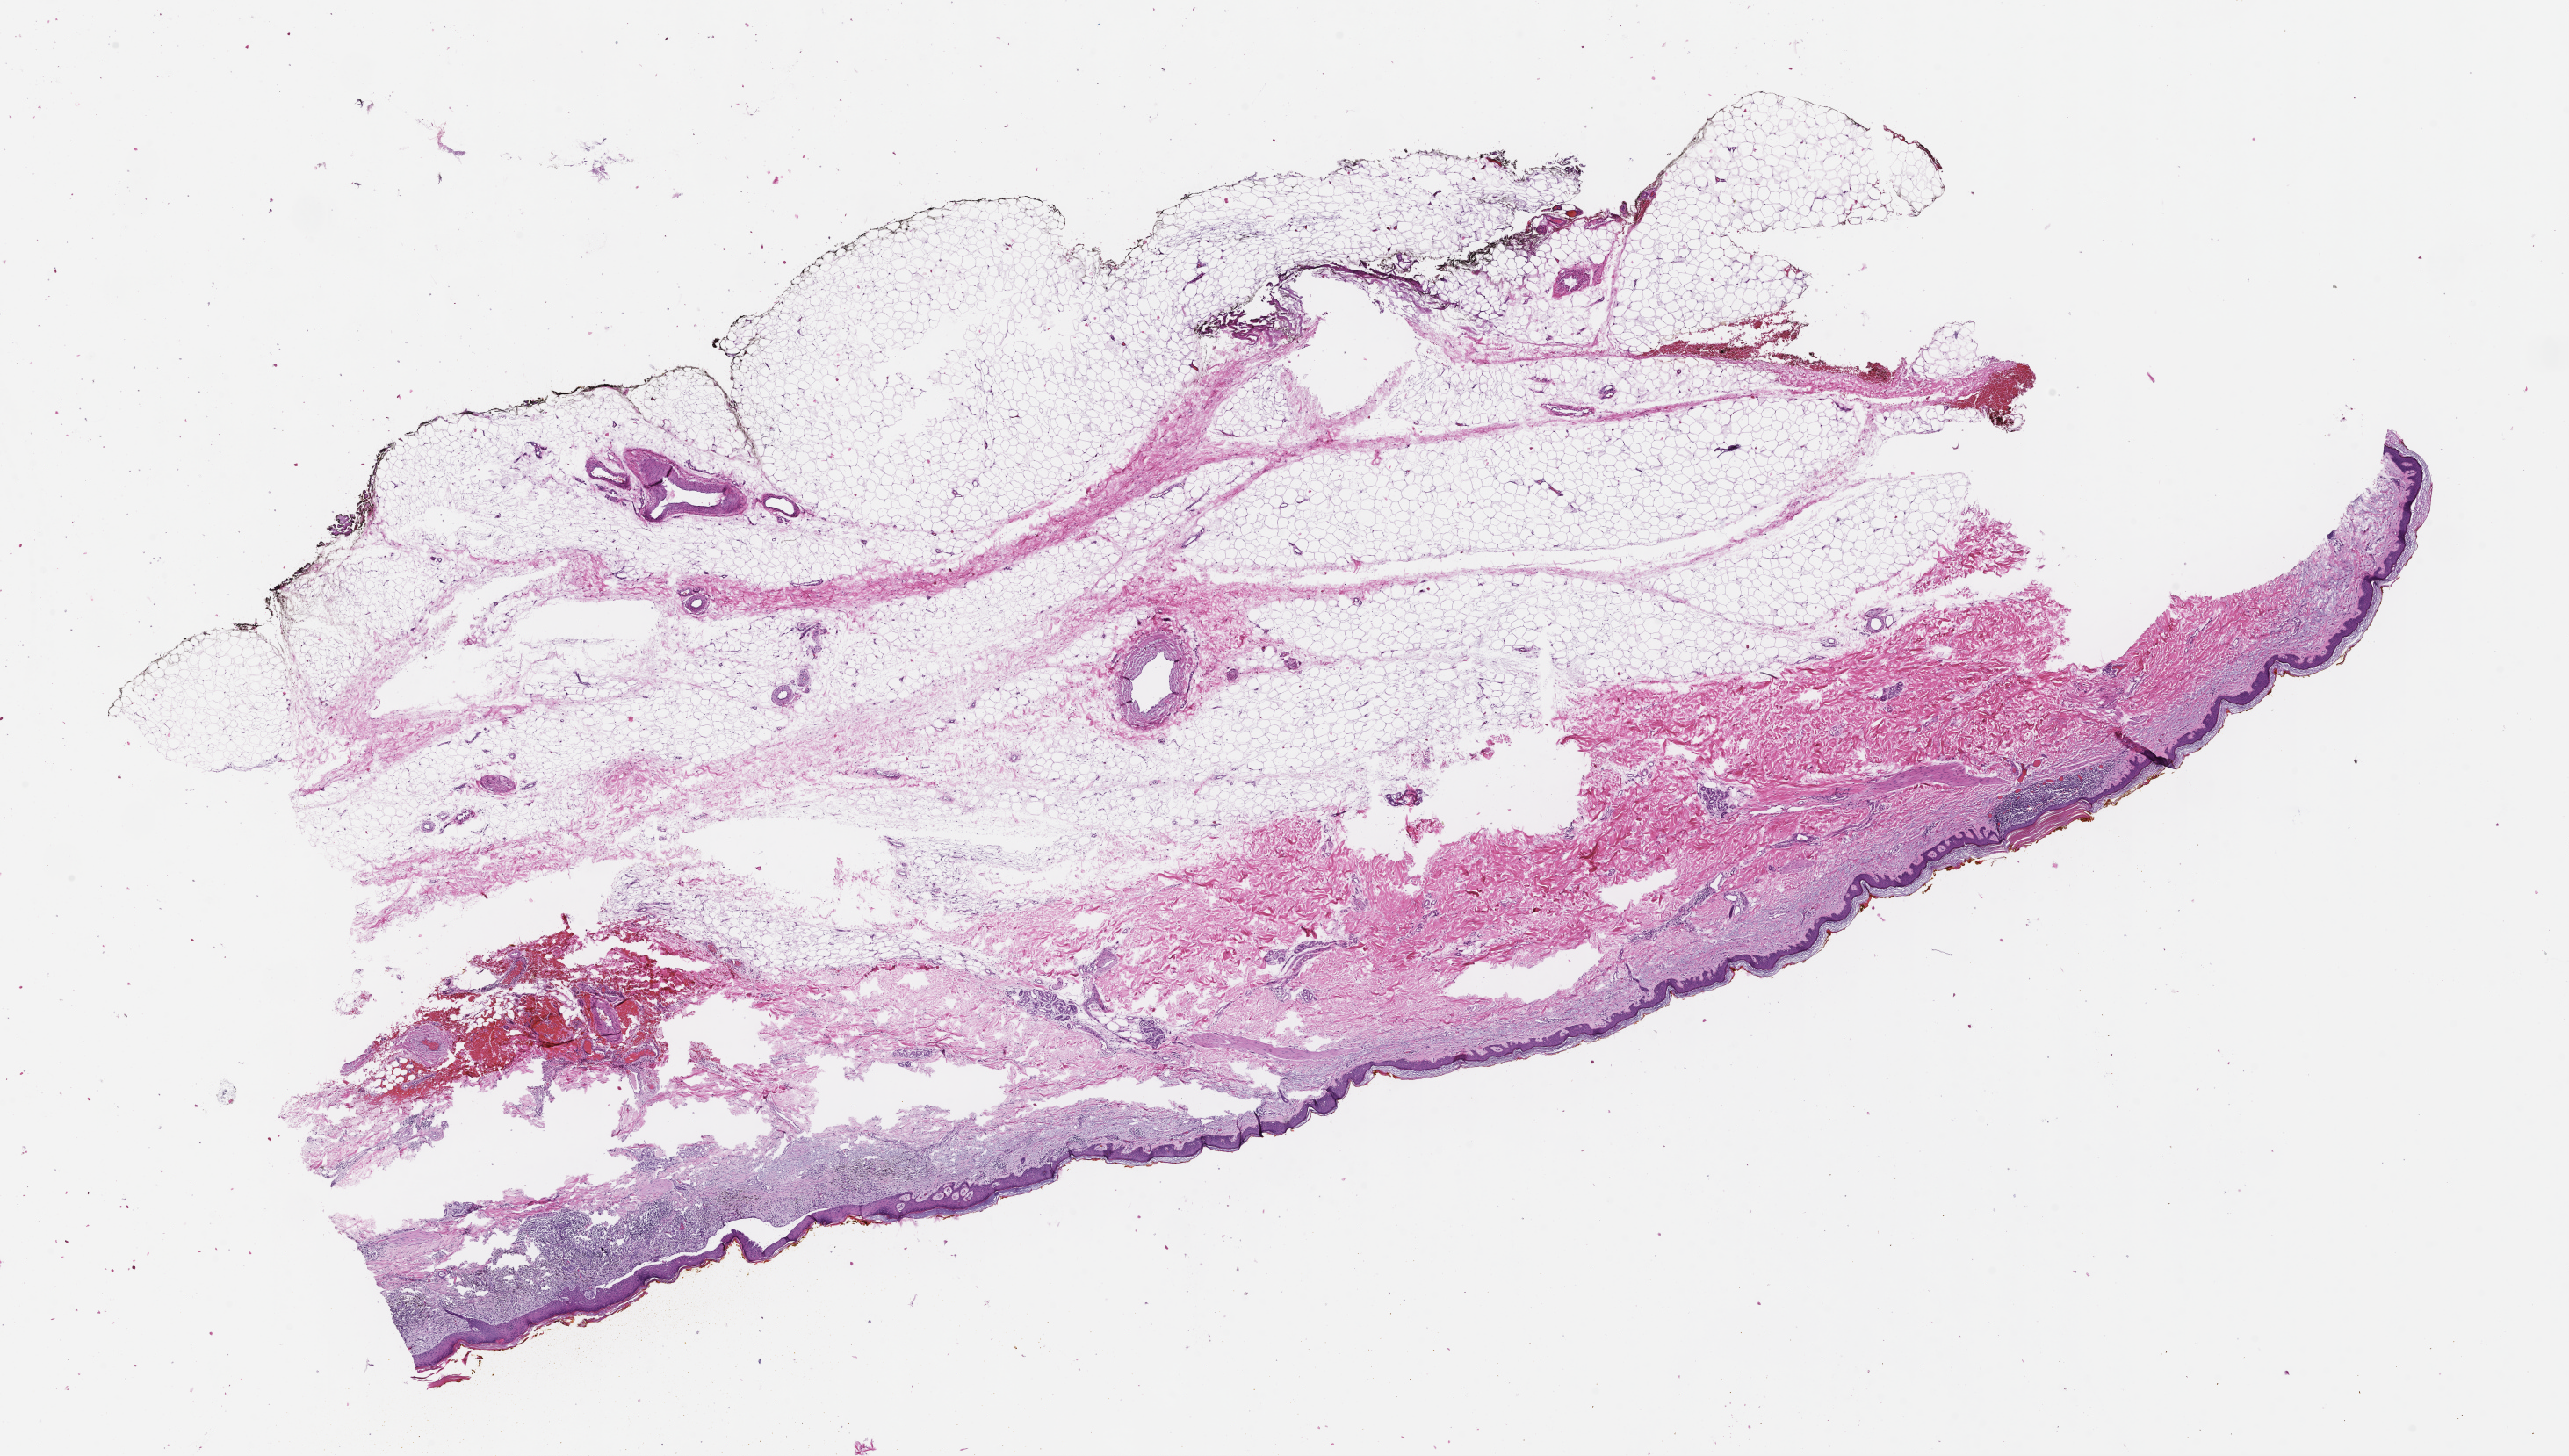
Whole-slide image, hematoxylin and eosin (H&E) stain, whole scanned area (about 23.6 x 13.4 mm) shown as a low-resolution overview, FFPE section, site: skin, specimen time point: archival tissue. Patient: male.
- this section: primary tumor
- diagnosis: Melanoma